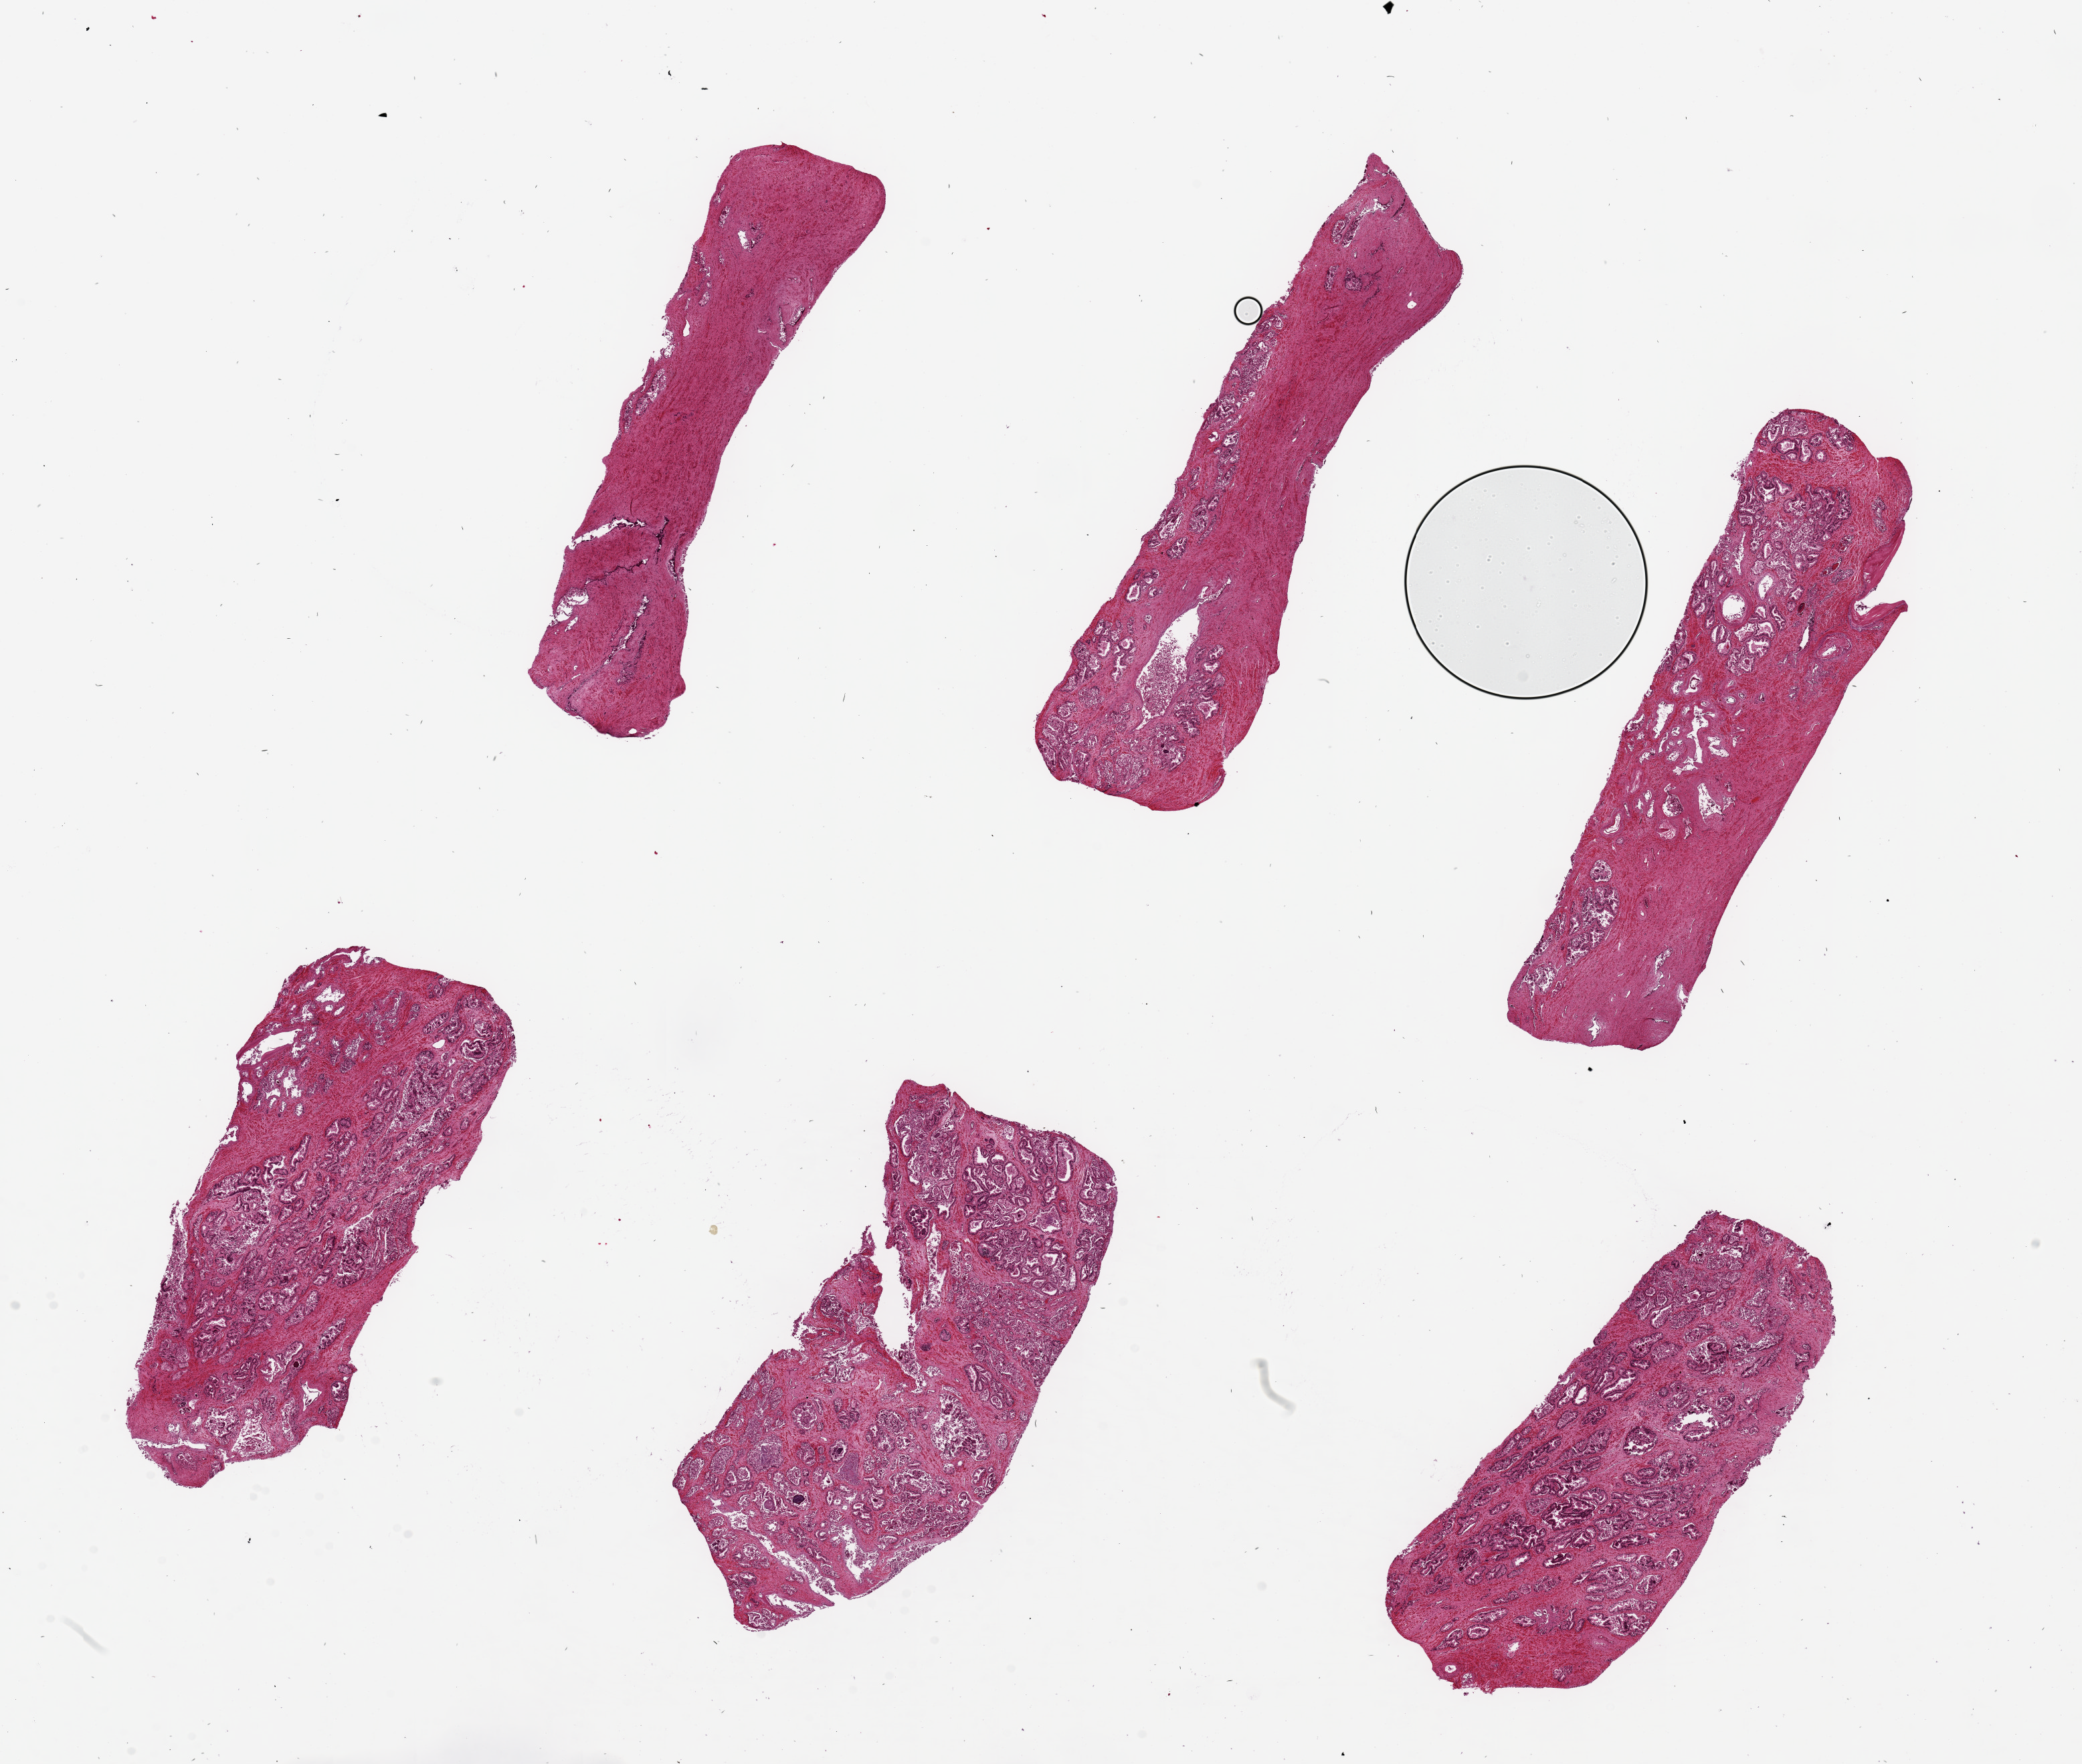
Digitized haematoxylin and eosin-stained section, brightfield, whole scanned area (about 24.6 x 20.9 mm) shown as a low-resolution overview. PAXgene-fixed, paraffin-embedded tissue. Target tissue: prostate. Tissue donor sample. Male donor.
Pathologist's review note for this sample: 6 pieces, up to 8x2mm; variable amounts of stroma and hyperplastic glands.